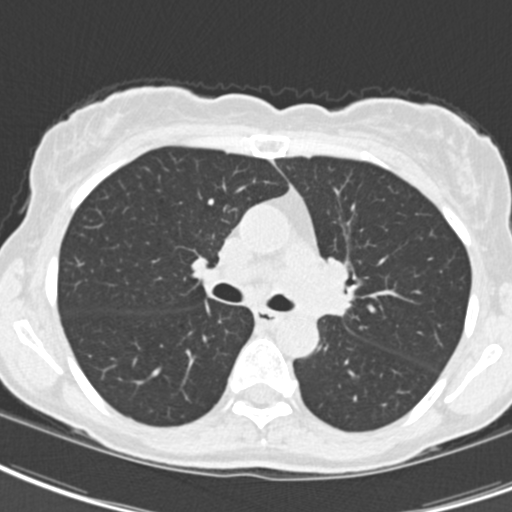
Chest CT (low-dose screening protocol), one axial image, baseline screening round, lung window (W 1500 / L -600 HU), 2 mm slice thickness, 120 kVp, slice 65 of 189 in the series. Female participant, aged 62 years at enrolment. Current smoker at enrolment.
Expert reader's lesion annotation, bounding box <295,247,370,330> (left, top, right, bottom; pixels). Screening reader's record for this exam (one nodule recorded; not confirmed to be the boxed lesion): non-calcified nodule or mass ≥4 mm, right upper lobe, 24 × 20 mm, smooth margins, ground glass attenuation. Note: the box lies in the patient's left hemithorax on this image, whereas the reader's record names the right lung; they may be different findings. Official screen result: positive, change unspecified: nodule(s) >= 4 mm or enlarging nodule(s), mass(es), or other non-specific abnormalities suspicious for lung cancer. Lung cancer was diagnosed 24 days after this screen: oat cell carcinoma, left hilum, left main stem bronchus, stage IIIB (AJCC 6th edition), 50 mm at pathology.